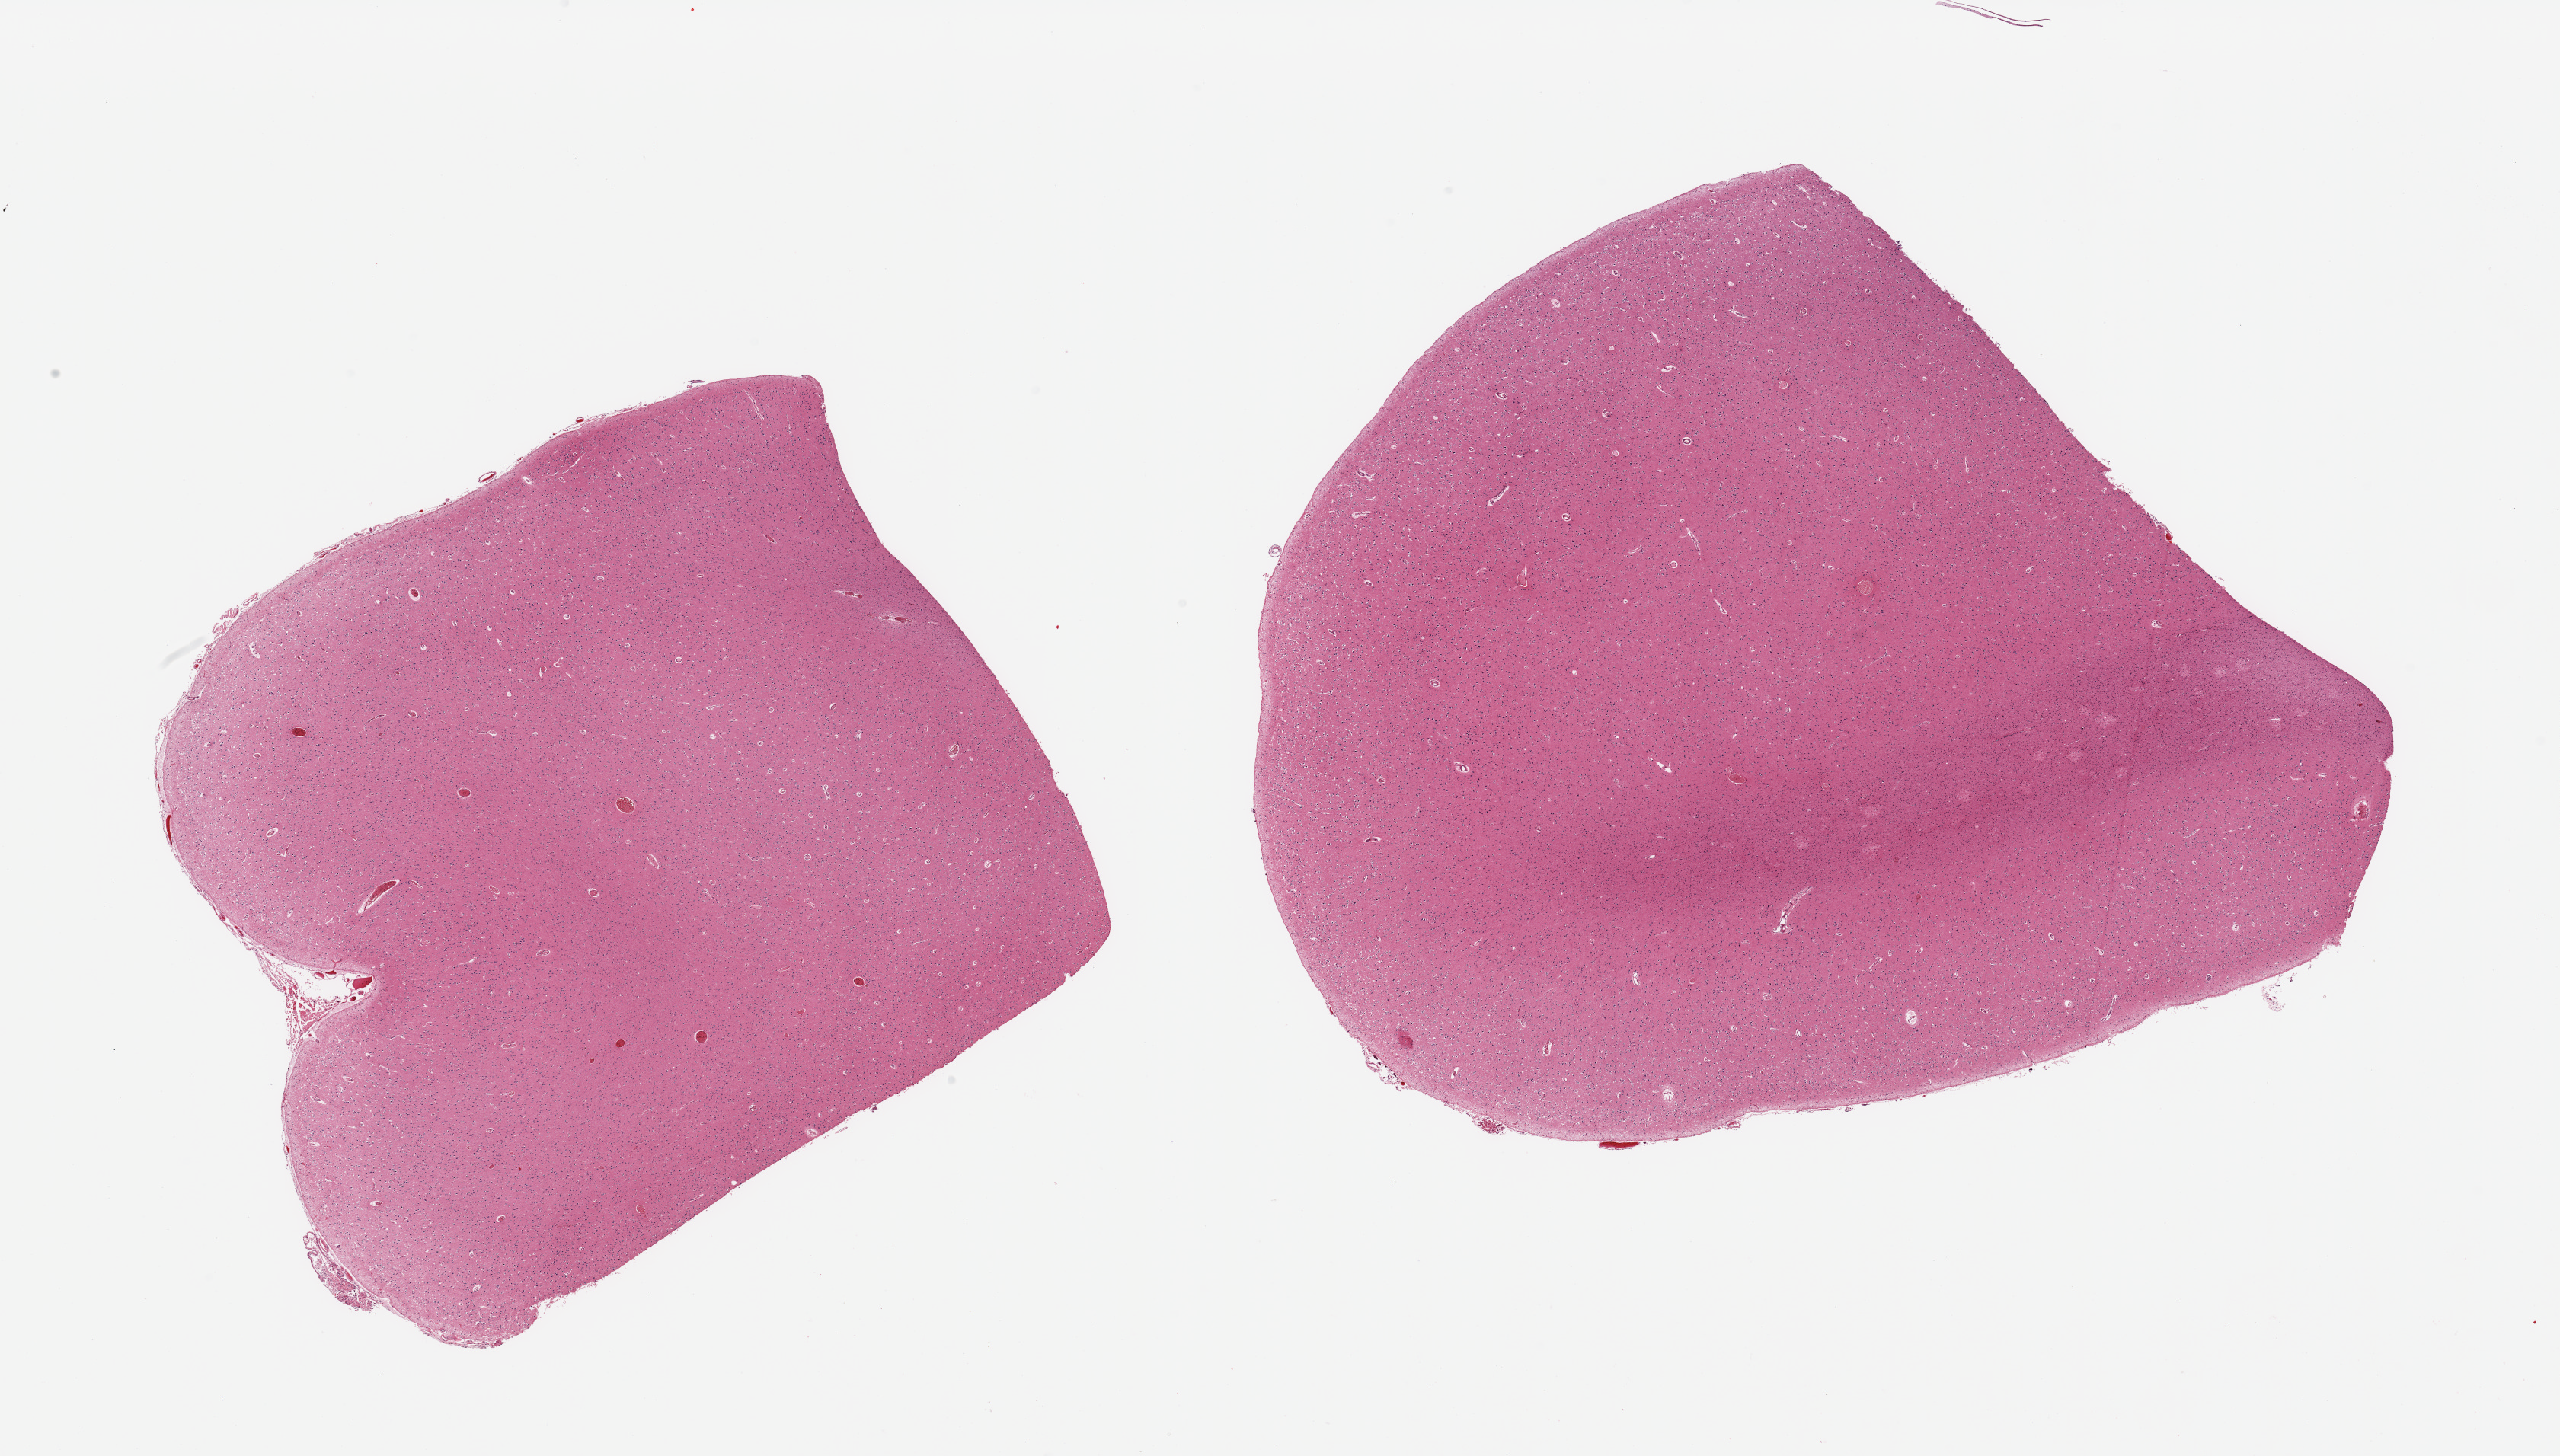
Digitized haematoxylin and eosin-stained section, shown as a low-resolution overview of the whole scanned area (about 26.6 x 15.1 mm). PAXgene-fixed paraffin-embedded (PFPE) section. Target tissue: cerebral cortex. Donor tissue sample. Donor: male.
- review note (as recorded): 2 pieces, no abnormalities